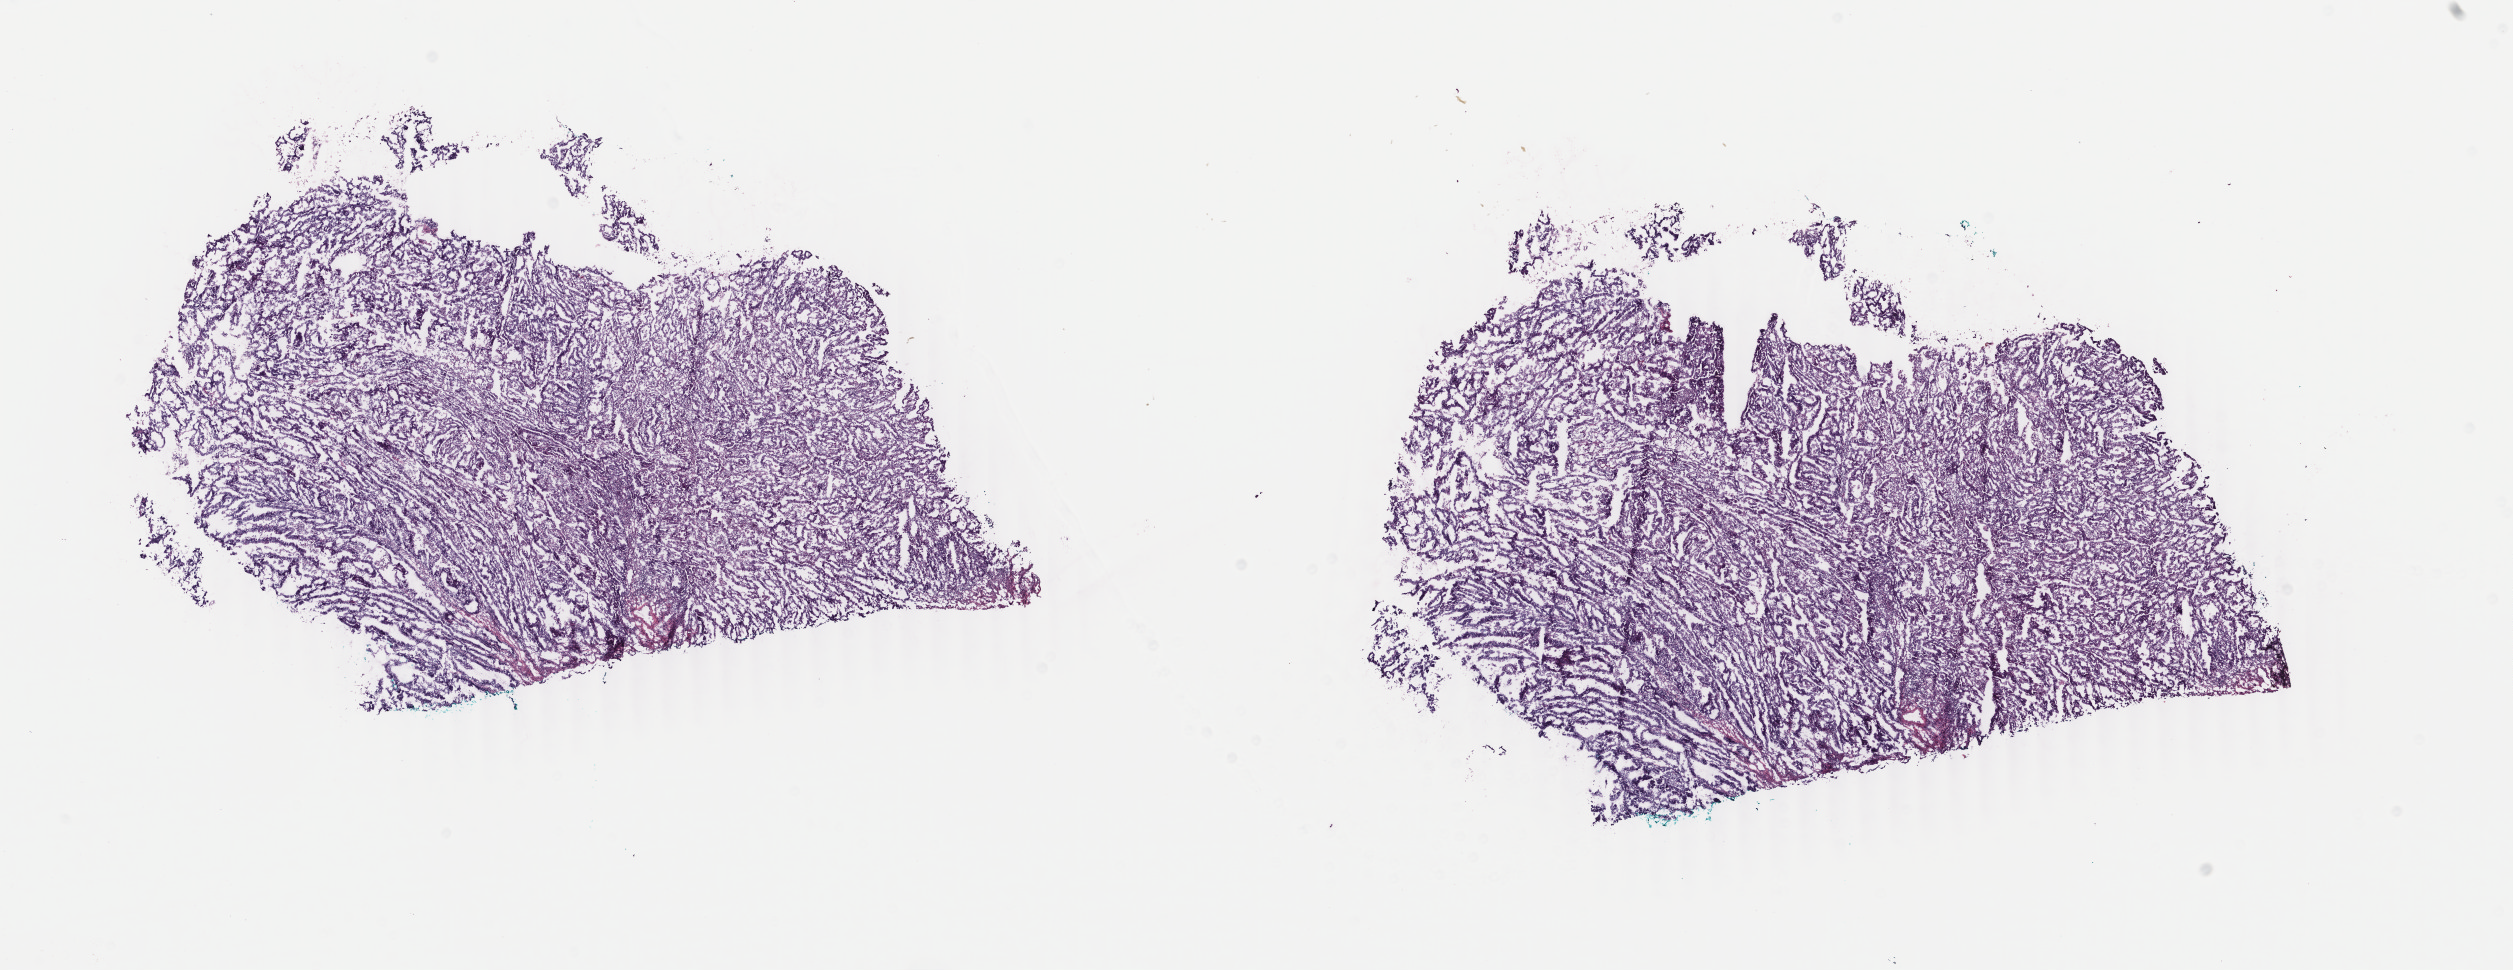
Digitized H&E tissue section (whole slide) — a low-resolution overview of the entire scanned area, about 20.0 x 7.7 mm. Frozen section from the top of the tissue portion. Primary tumour sample from the uterus. Female, age 65 years at initial diagnosis. Histologic grade: G1 (well differentiated). Composition of this section per pathologist review: tumour cells 80%, tumour nuclei 80%, normal cells 0%, stromal cells 20%, necrosis 0%. Infiltration values recorded for this section: lymphocyte infiltration 40%, monocyte infiltration 10%, neutrophil infiltration 20%.
Diagnosis: Endometrioid adenocarcinoma, NOS. FIGO stage: IB.